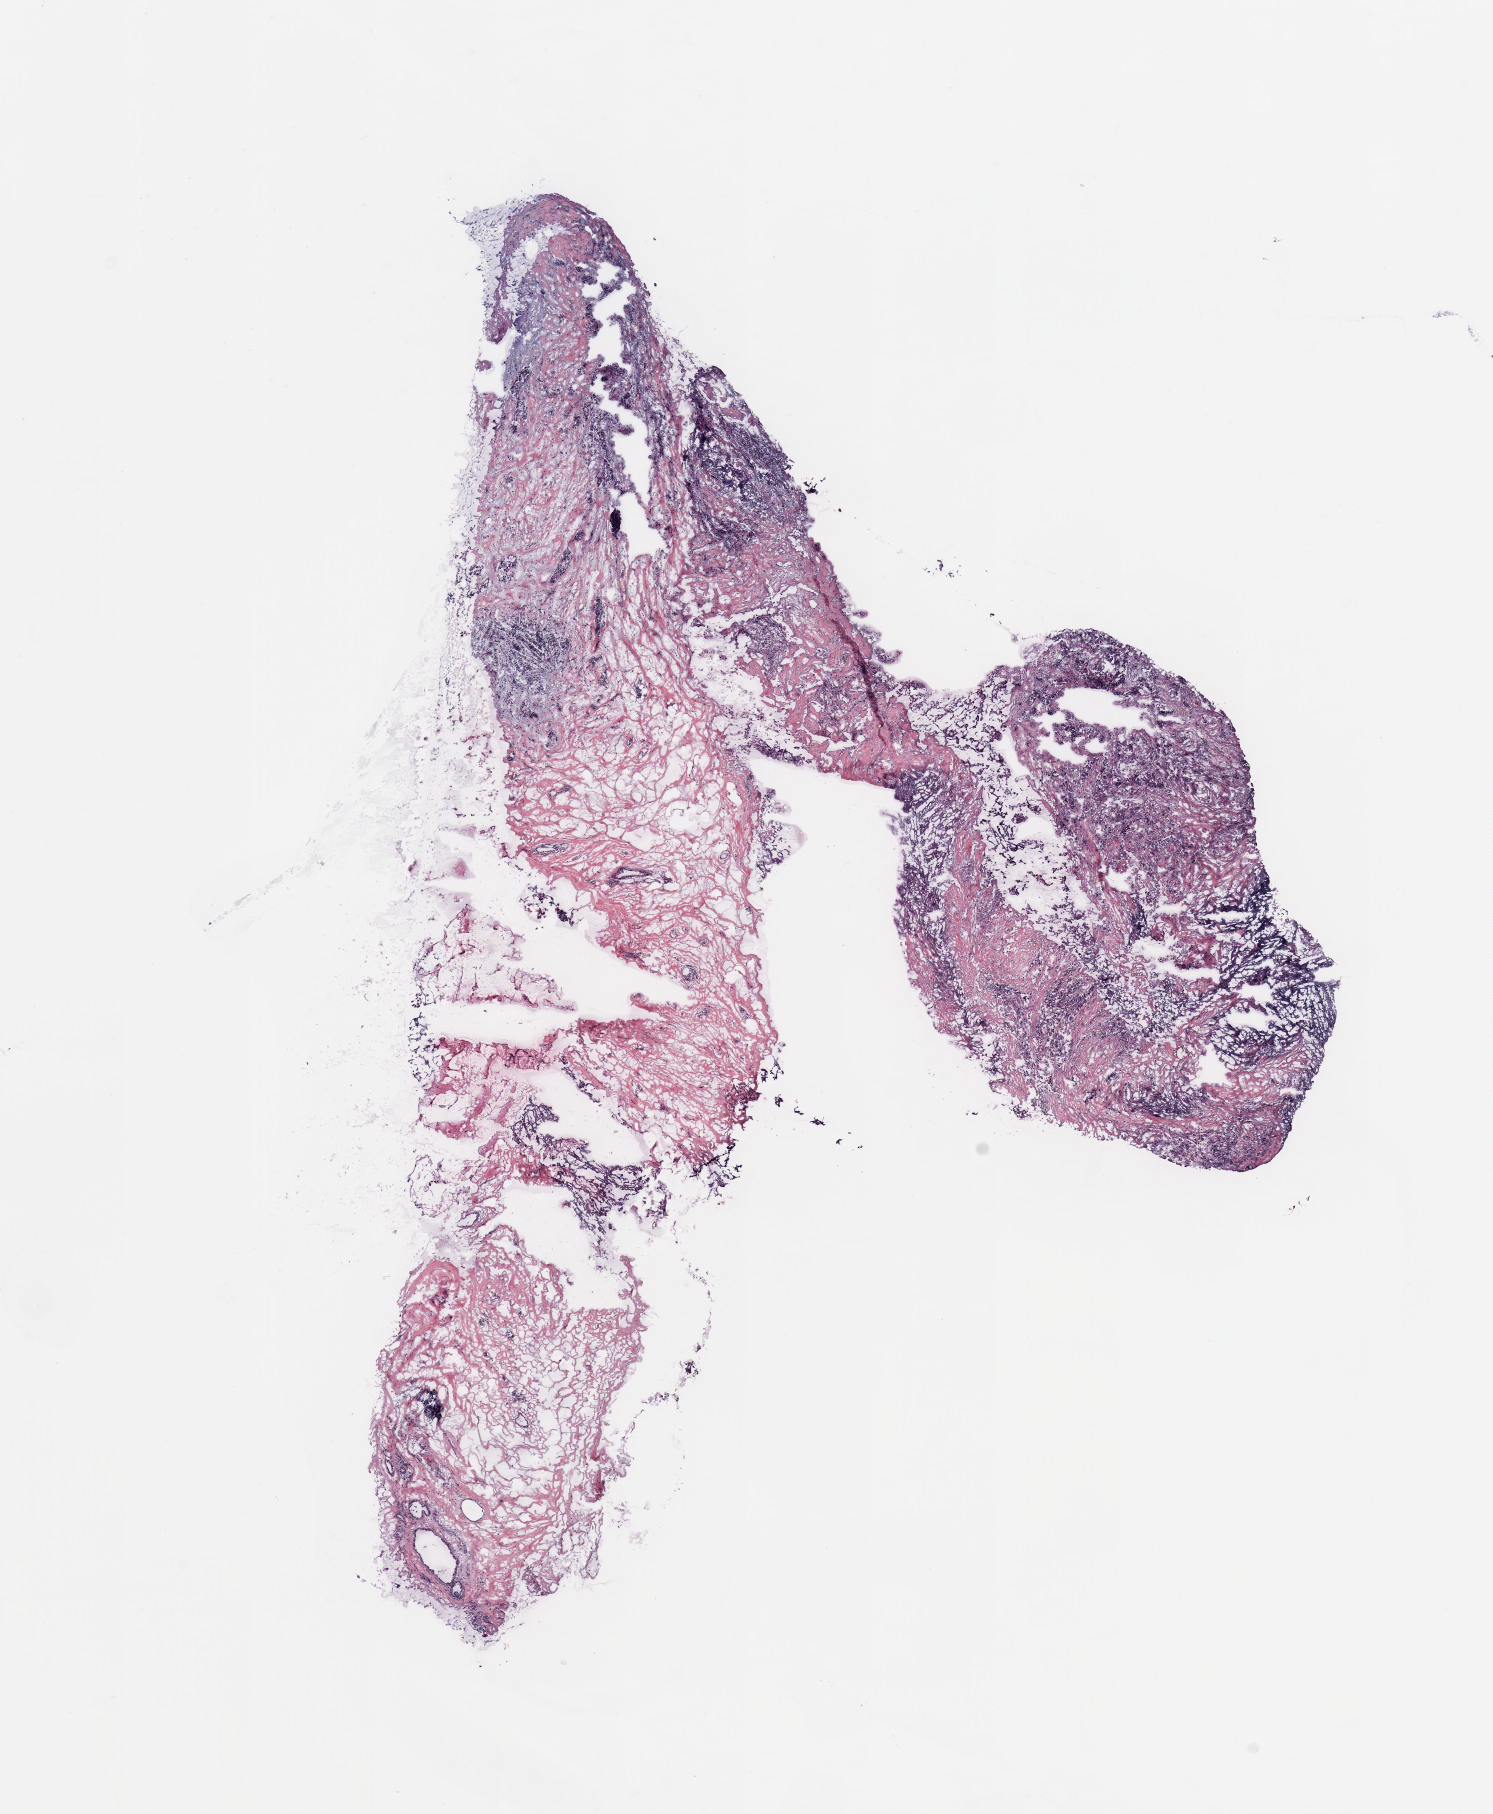
H&E whole-slide image, low-resolution overview of the scanned area, about 11.8 x 14.4 mm, breast, tissue type not recorded.
* patient diagnosis (cohort enrolment): breast cancer (breast)